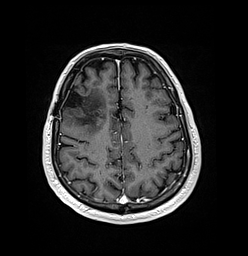
Brain MRI from a brain-tumour surgery series, one axial slice; position 49 of 176 along the scan axis; T1-weighted post-contrast; 1 mm slice thickness; 248 × 256 image matrix. From the clinical record (not read from this slice): histopathology: Oligodendroglioma; WHO grade: 3; IDH mutation: yes; tumour location: Right Frontal.
Structures marked on this image (outlined manually by an expert reader):
- previous resection cavity: bounding box [x1, y1, x2, y2] px = [63, 86, 84, 108]